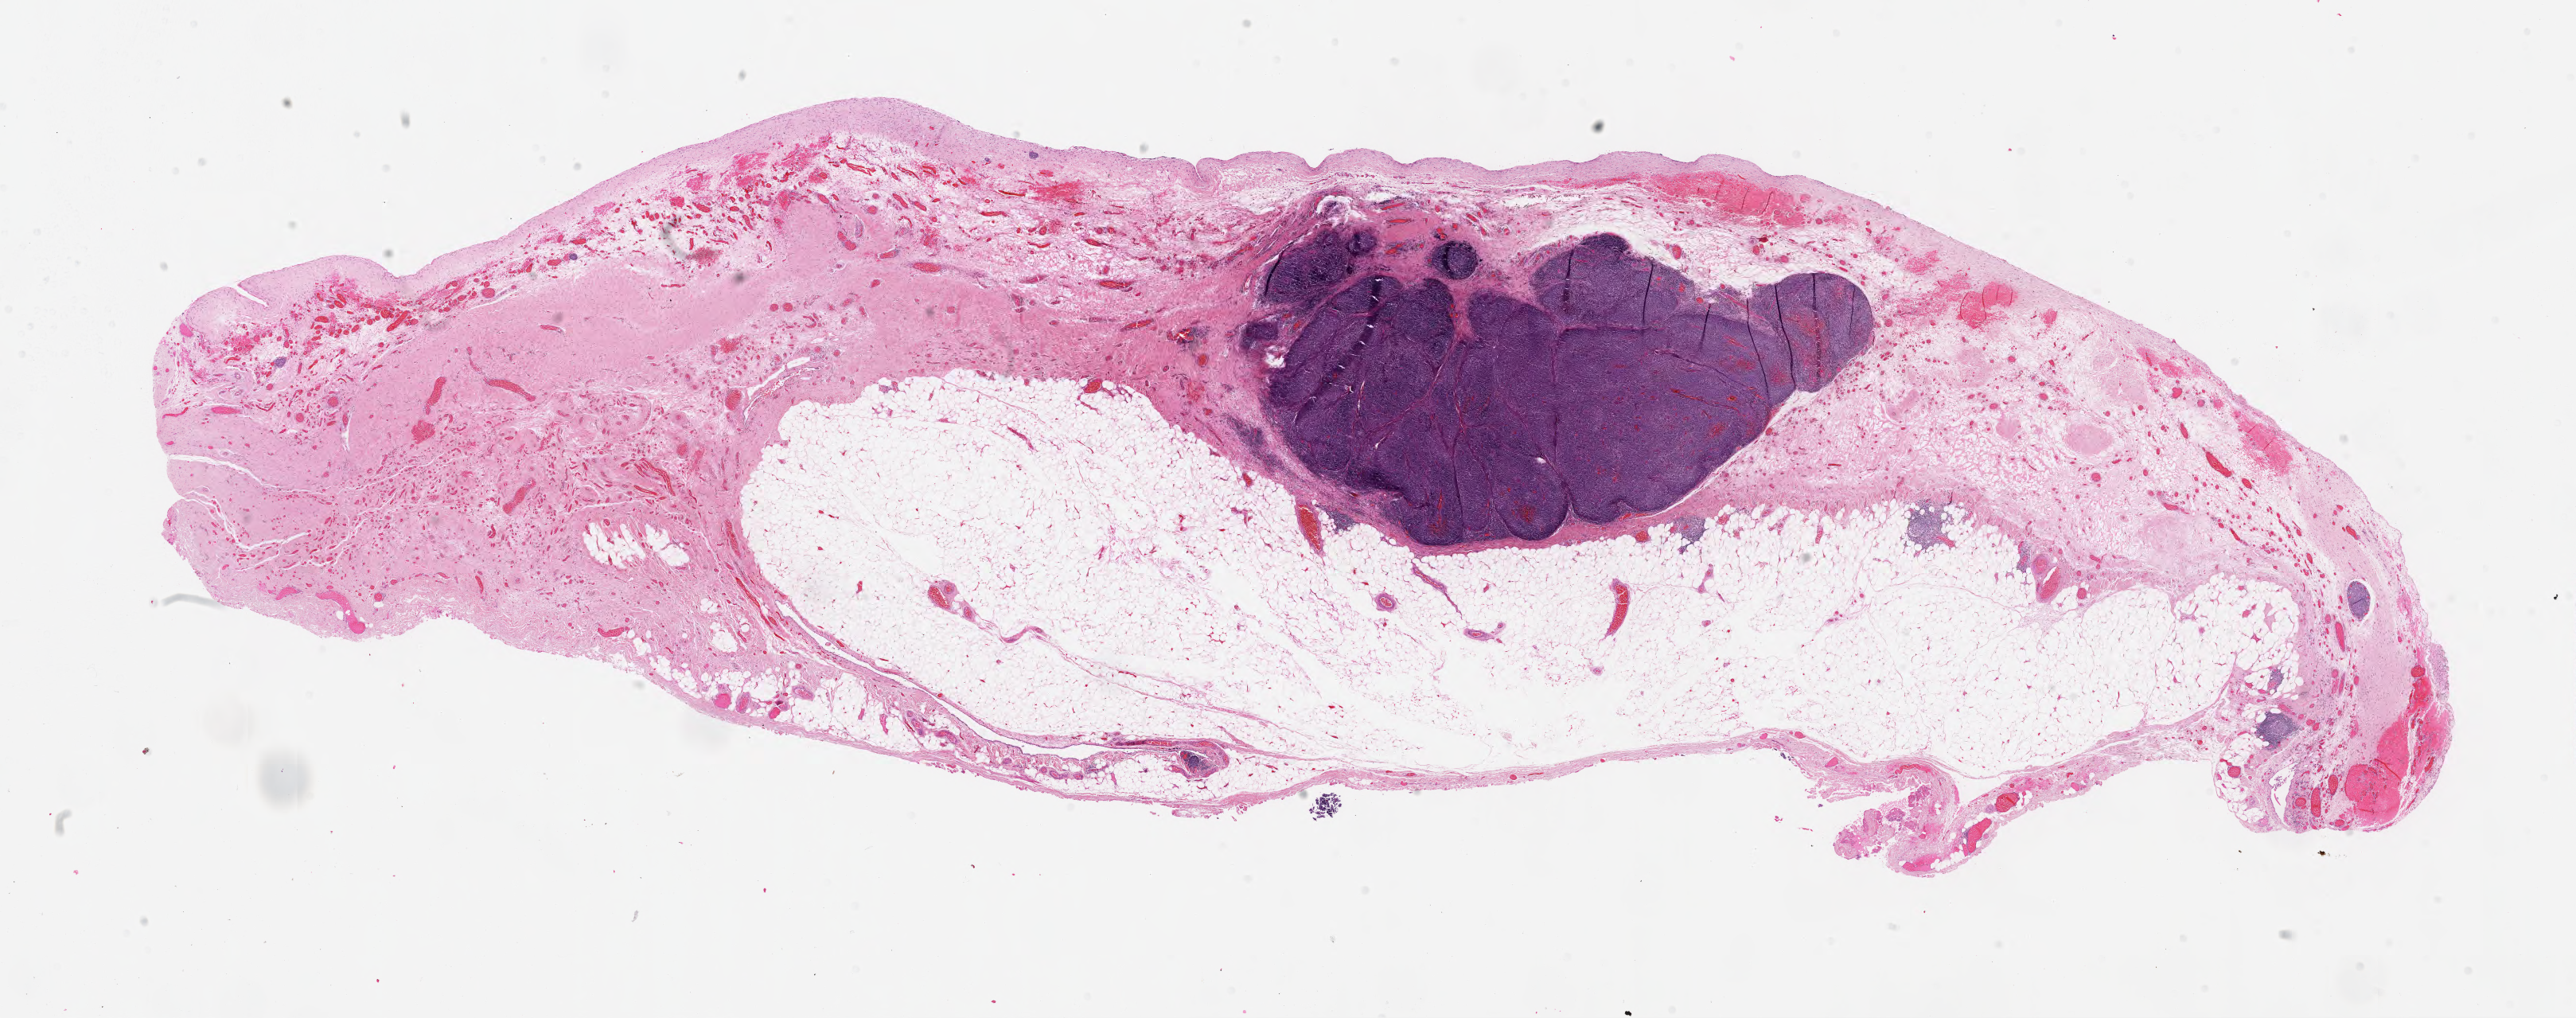
Whole-slide histology image, H&E-stained — low-resolution overview of the scanned area, about 26.2 x 10.3 mm (acquisition: 40x scan). Formalin-fixed paraffin-embedded (FFPE) diagnostic section. Thymus, primary tumour sample. Male patient; age at initial diagnosis 45 years.
- histologic diagnosis: Thymoma, type B1, malignant